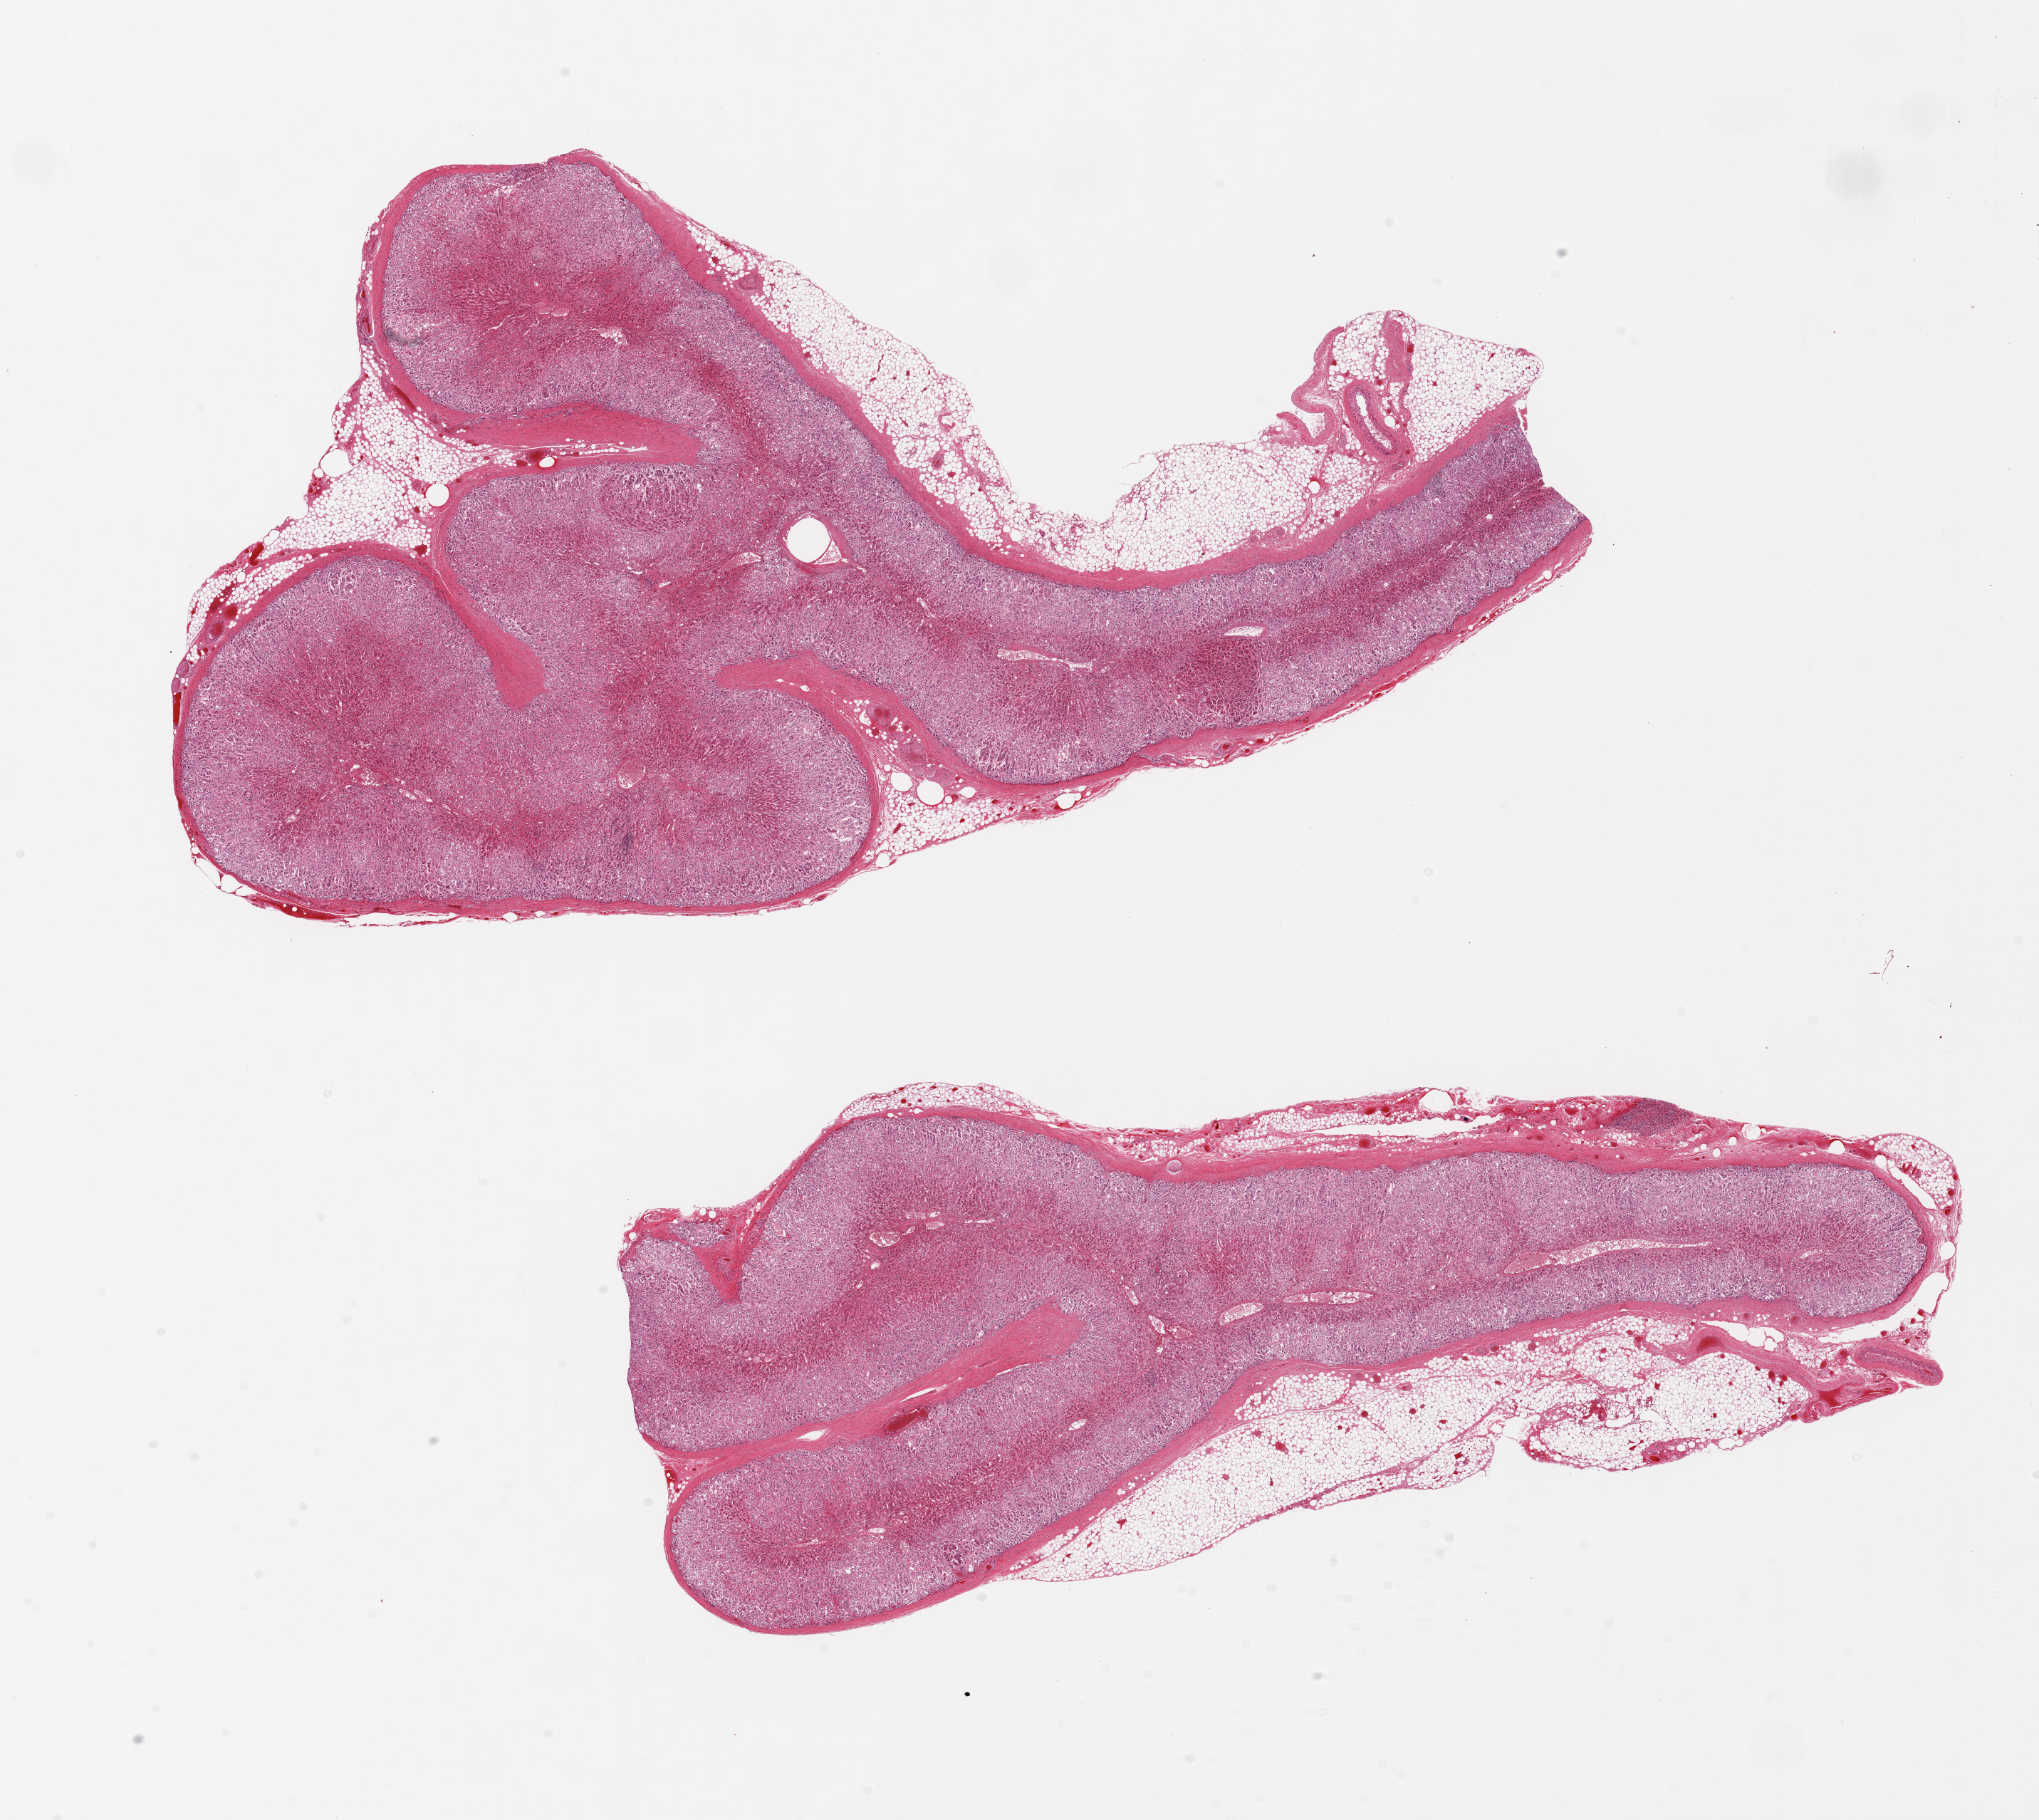
Whole-slide image, H&E stain, shown as a low-resolution overview of the whole scanned area (about 22.6 x 20.2 mm, from a 20x scan), PAXgene-fixed paraffin-embedded (PFPE) section, section of adrenal gland (target tissue), donor tissue sample.
Reviewer comment on this tissue sample: 2 pieces ~ 15x6mm, all cortex, discontinuous adherent fat up to 1.5mm.